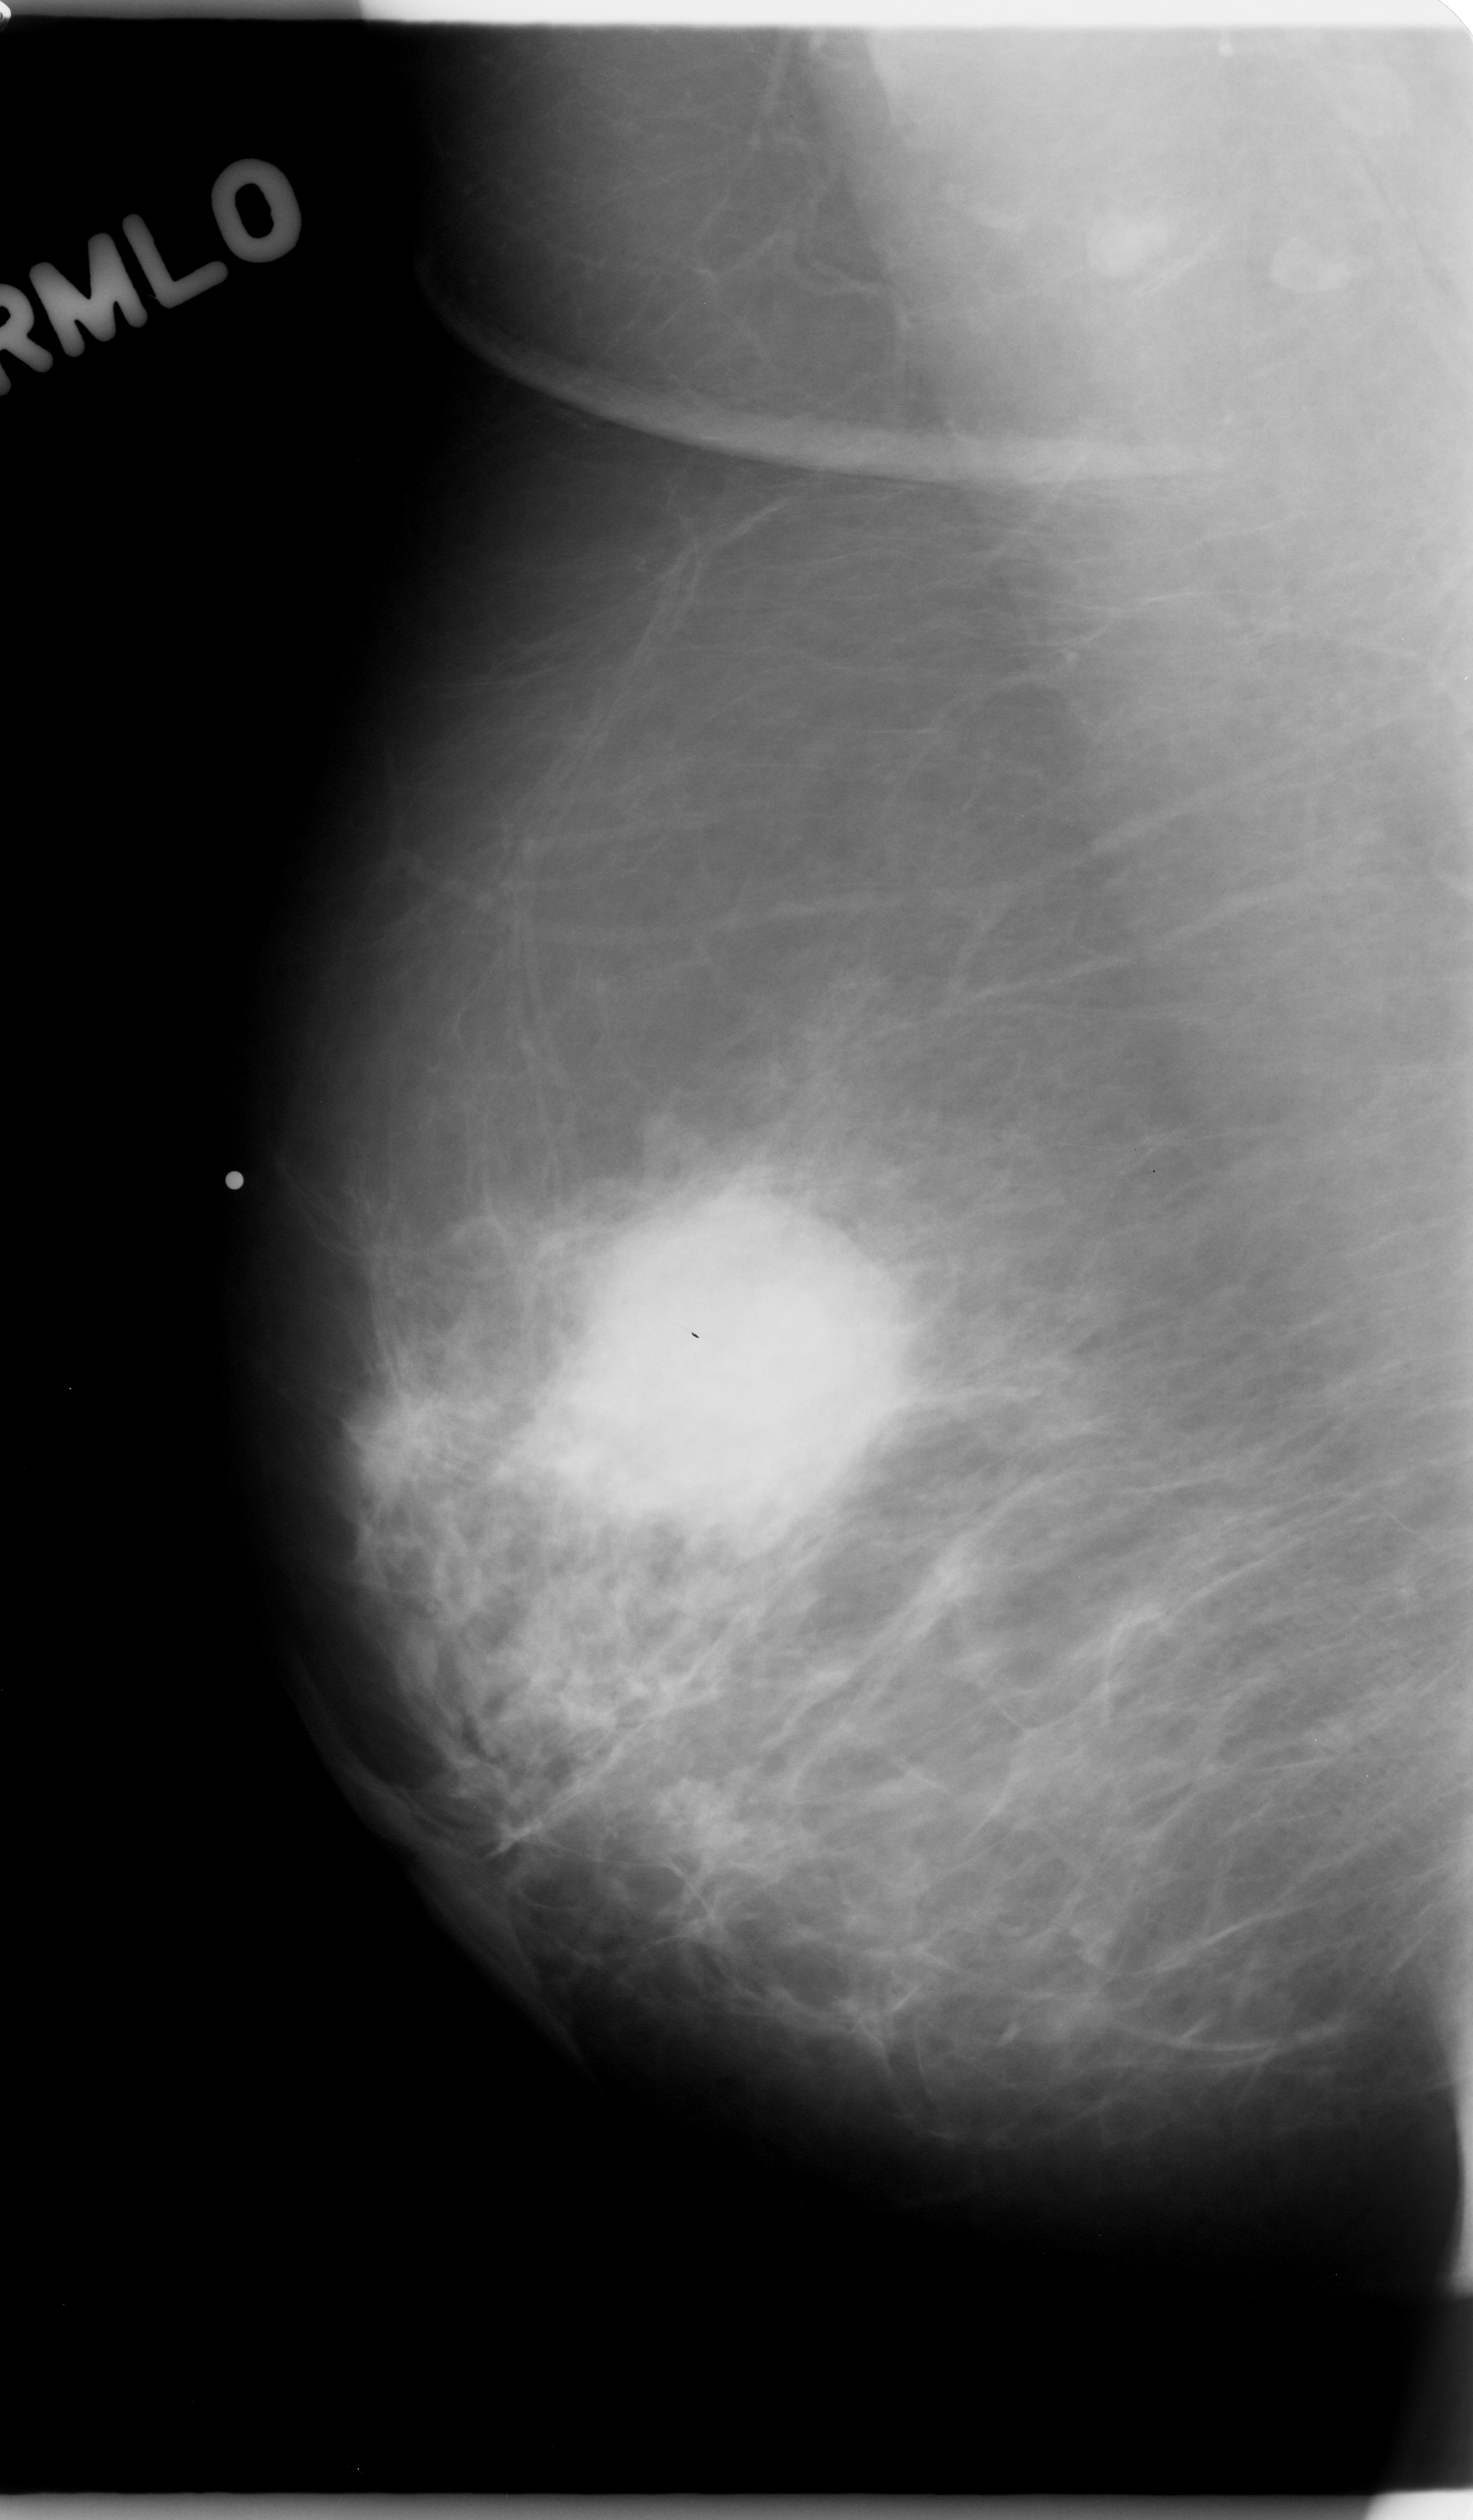
Digitized screen-film mammogram, right breast, mediolateral oblique (MLO) view, breast composition: almost entirely fatty (BI-RADS density category 1 of 4).
- Marked abnormality: mass, shape lobulated, margins microlobulated; BI-RADS assessment category 5; pathology (as recorded): malignant.